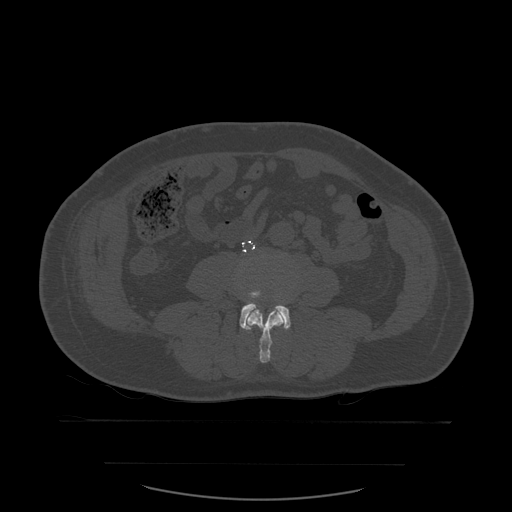
CT including the spine, one axial slice. Position 179 of 590 along the scan axis. Bone window (W 1800 / L 400 HU). 1.25 mm slice thickness. 512 × 512 image matrix, field of view 479 × 479 mm. Patient age 71 years. Case-level facts recorded for this patient, not image findings: primary cancer: lung.
Annotated regions visible in this slice (semi-automatically segmented with operator editing):
- L3 vertebra: bounding box (x1, y1, x2, y2) in pixels: (248, 310, 285, 363)
- L4 vertebra: (240, 292, 291, 330)